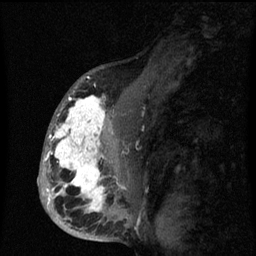
Breast MRI (dynamic contrast-enhanced), one sagittal slice; position 38 of 60 along the scan axis; dynamic contrast-enhanced series, image 2 of 3 at this slice position (ordered by acquisition); 1.5 T; TE 4.2 ms, TR 8 ms; 2 mm slice thickness; 256 × 256 image matrix, field of view 190 × 190 mm. Patient: female, 50 years.
Outlined on this slice (semi-automatic segmentation, software-assisted and operator-edited):
- analysis volume of interest (the breast-tissue region the enhancement analysis was run in; not a lesion): box from (x=43, y=90) to (x=142, y=216) px
- tumour enhancement mask (voxels above the 70 % enhancement threshold inside the analysis volume of interest): (x=44, y=91)–(x=126, y=211)